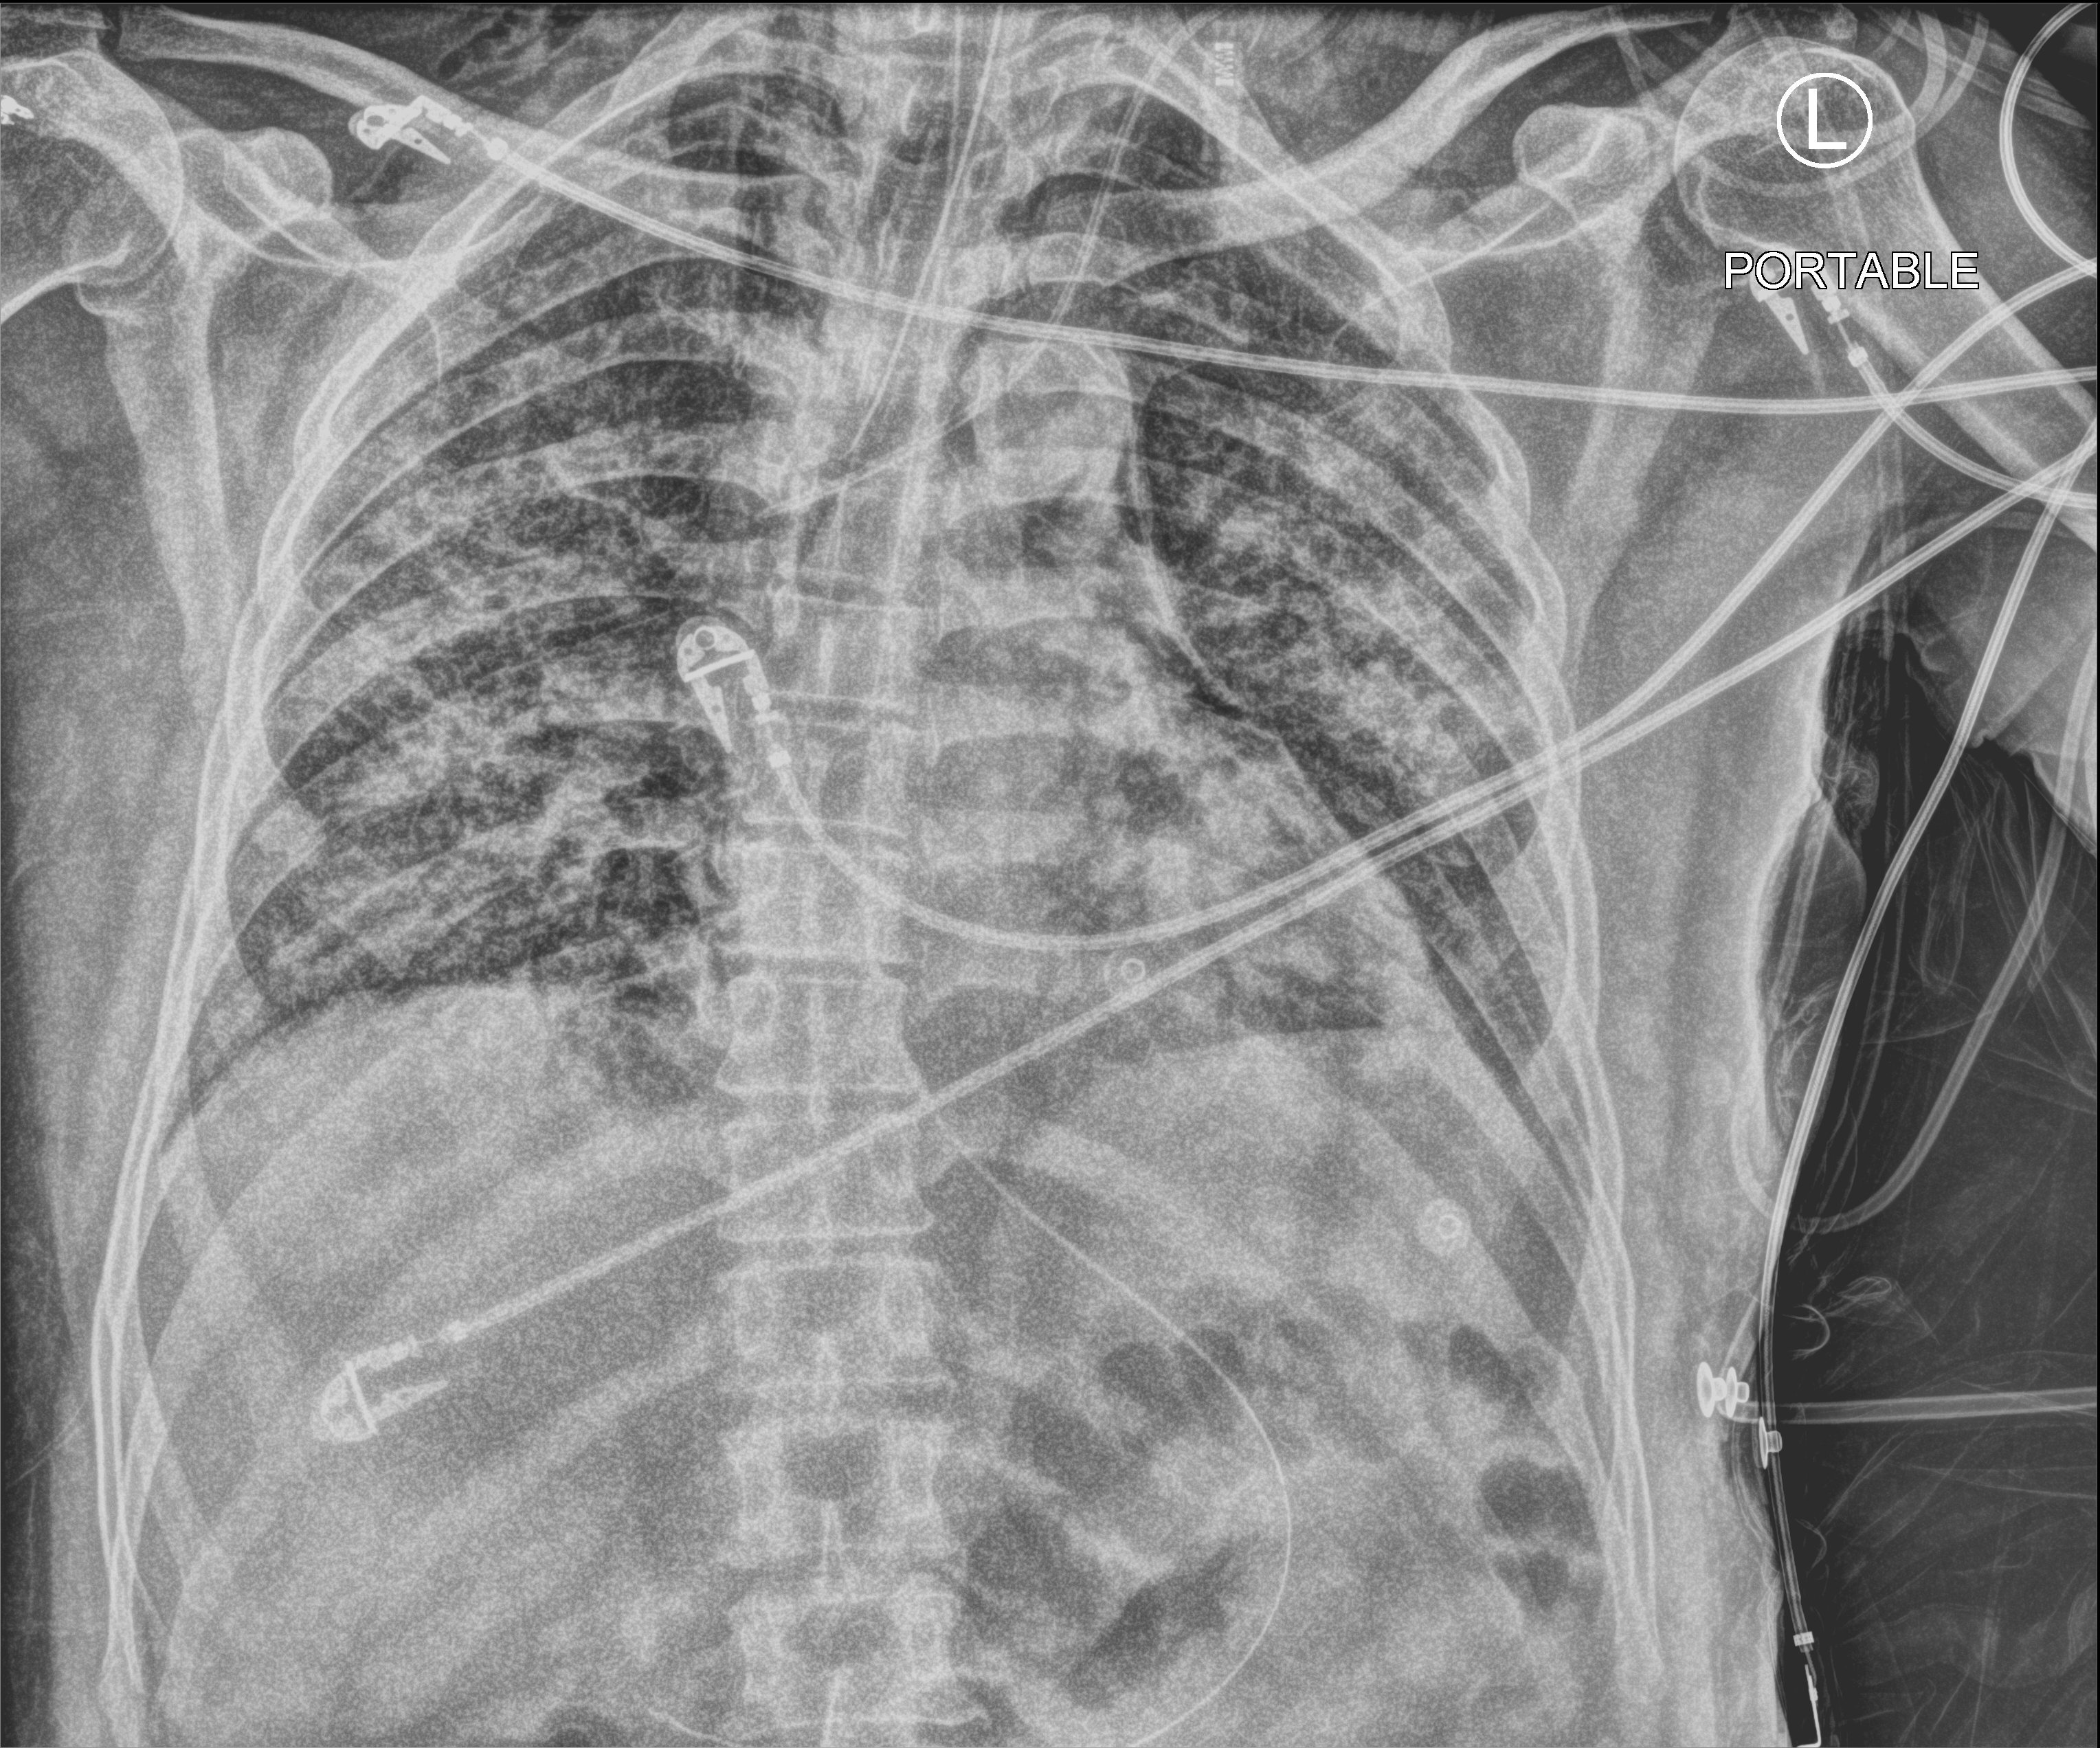
Bedside chest radiograph (computed radiography); anteroposterior (AP) projection. Male patient hospitalised with COVID-19, age 60–74 years.
Admission-level facts for this patient (not findings on this image; timing relative to this image not recorded):
- mechanically ventilated during this hospital stay: yes
- hypertension (admission record): no
- length of hospital stay: 65 days